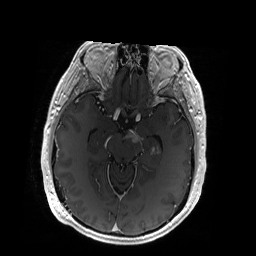
Brain MRI from a brain-tumour surgery series, one axial slice; position 114 of 192 along the scan axis; T1-weighted post-contrast; 256 × 256 image matrix, field of view 256 × 256 mm. From the clinical record (not read from this slice): histopathology: Glioblastoma; WHO grade: 4; IDH mutation: no.
Outlined on this slice (manually delineated by an expert):
- tumour: box from (x=126, y=130) to (x=160, y=154) px